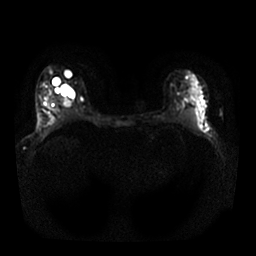
Breast MRI, one axial slice. Diffusion-weighted series; image 2 of 4 stored at this slice position (different b-values; order by instance number). 1.5 T. 256 × 256 image matrix. Female patient.
Annotated regions visible in this slice (expert manual segmentation):
- tumour on diffusion-weighted imaging: bounding box <190,80,201,99> (left, top, right, bottom; pixels)